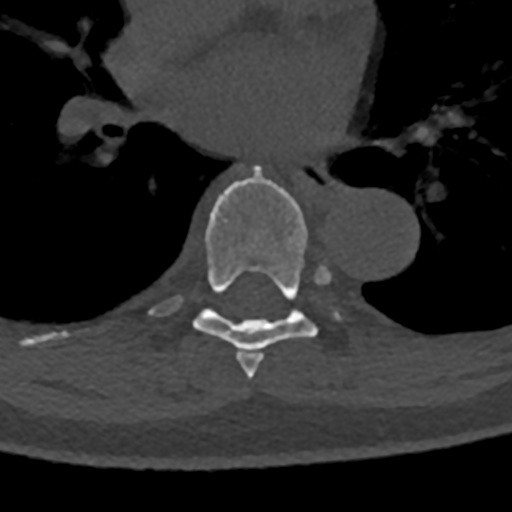
CT including the spine, one axial slice. Slice 762 of 797 in the series (ordered by position). 120 kVp. Bone window (W 1800 / L 400 HU). 0.5 mm slice thickness. 512 × 512 image matrix, field of view 160 × 160 mm. Male patient, age 74 years. Case-level facts recorded for this patient, not image findings: primary cancer: renal; vertebrae with lytic lesions (as recorded): T10, L1, L2, L3, L4, L5.
Structures marked on this image (semi-automatically segmented with operator editing):
- T6 vertebra: bounding box <245,354,264,379> (left, top, right, bottom; pixels)
- T7 vertebra: <149,166,345,370>